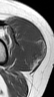
MRI of an extremity soft-tissue mass, one axial slice. Slice 29 of 42 in the series (ordered by position). MR volume resampled by the dataset authors to the PET/CT grid (not the native acquisition matrix). 3.27 mm slice thickness. 54 × 97 image matrix, field of view 53 × 95 mm. Female patient. From the clinical record (not read from this slice): histological type: spindle cell suggestive of biphasic synovial sarcoma; grade: intermediate; site of the primary tumour: left knee.
Annotated regions visible in this slice (expert contour drawn on MRI and transferred to this co-registered scan by the dataset authors):
- gross tumour volume including surrounding oedema: bounding box (x1, y1, x2, y2) in pixels: (21, 23, 45, 63)
- gross tumour volume (mass): (21, 23, 45, 63)